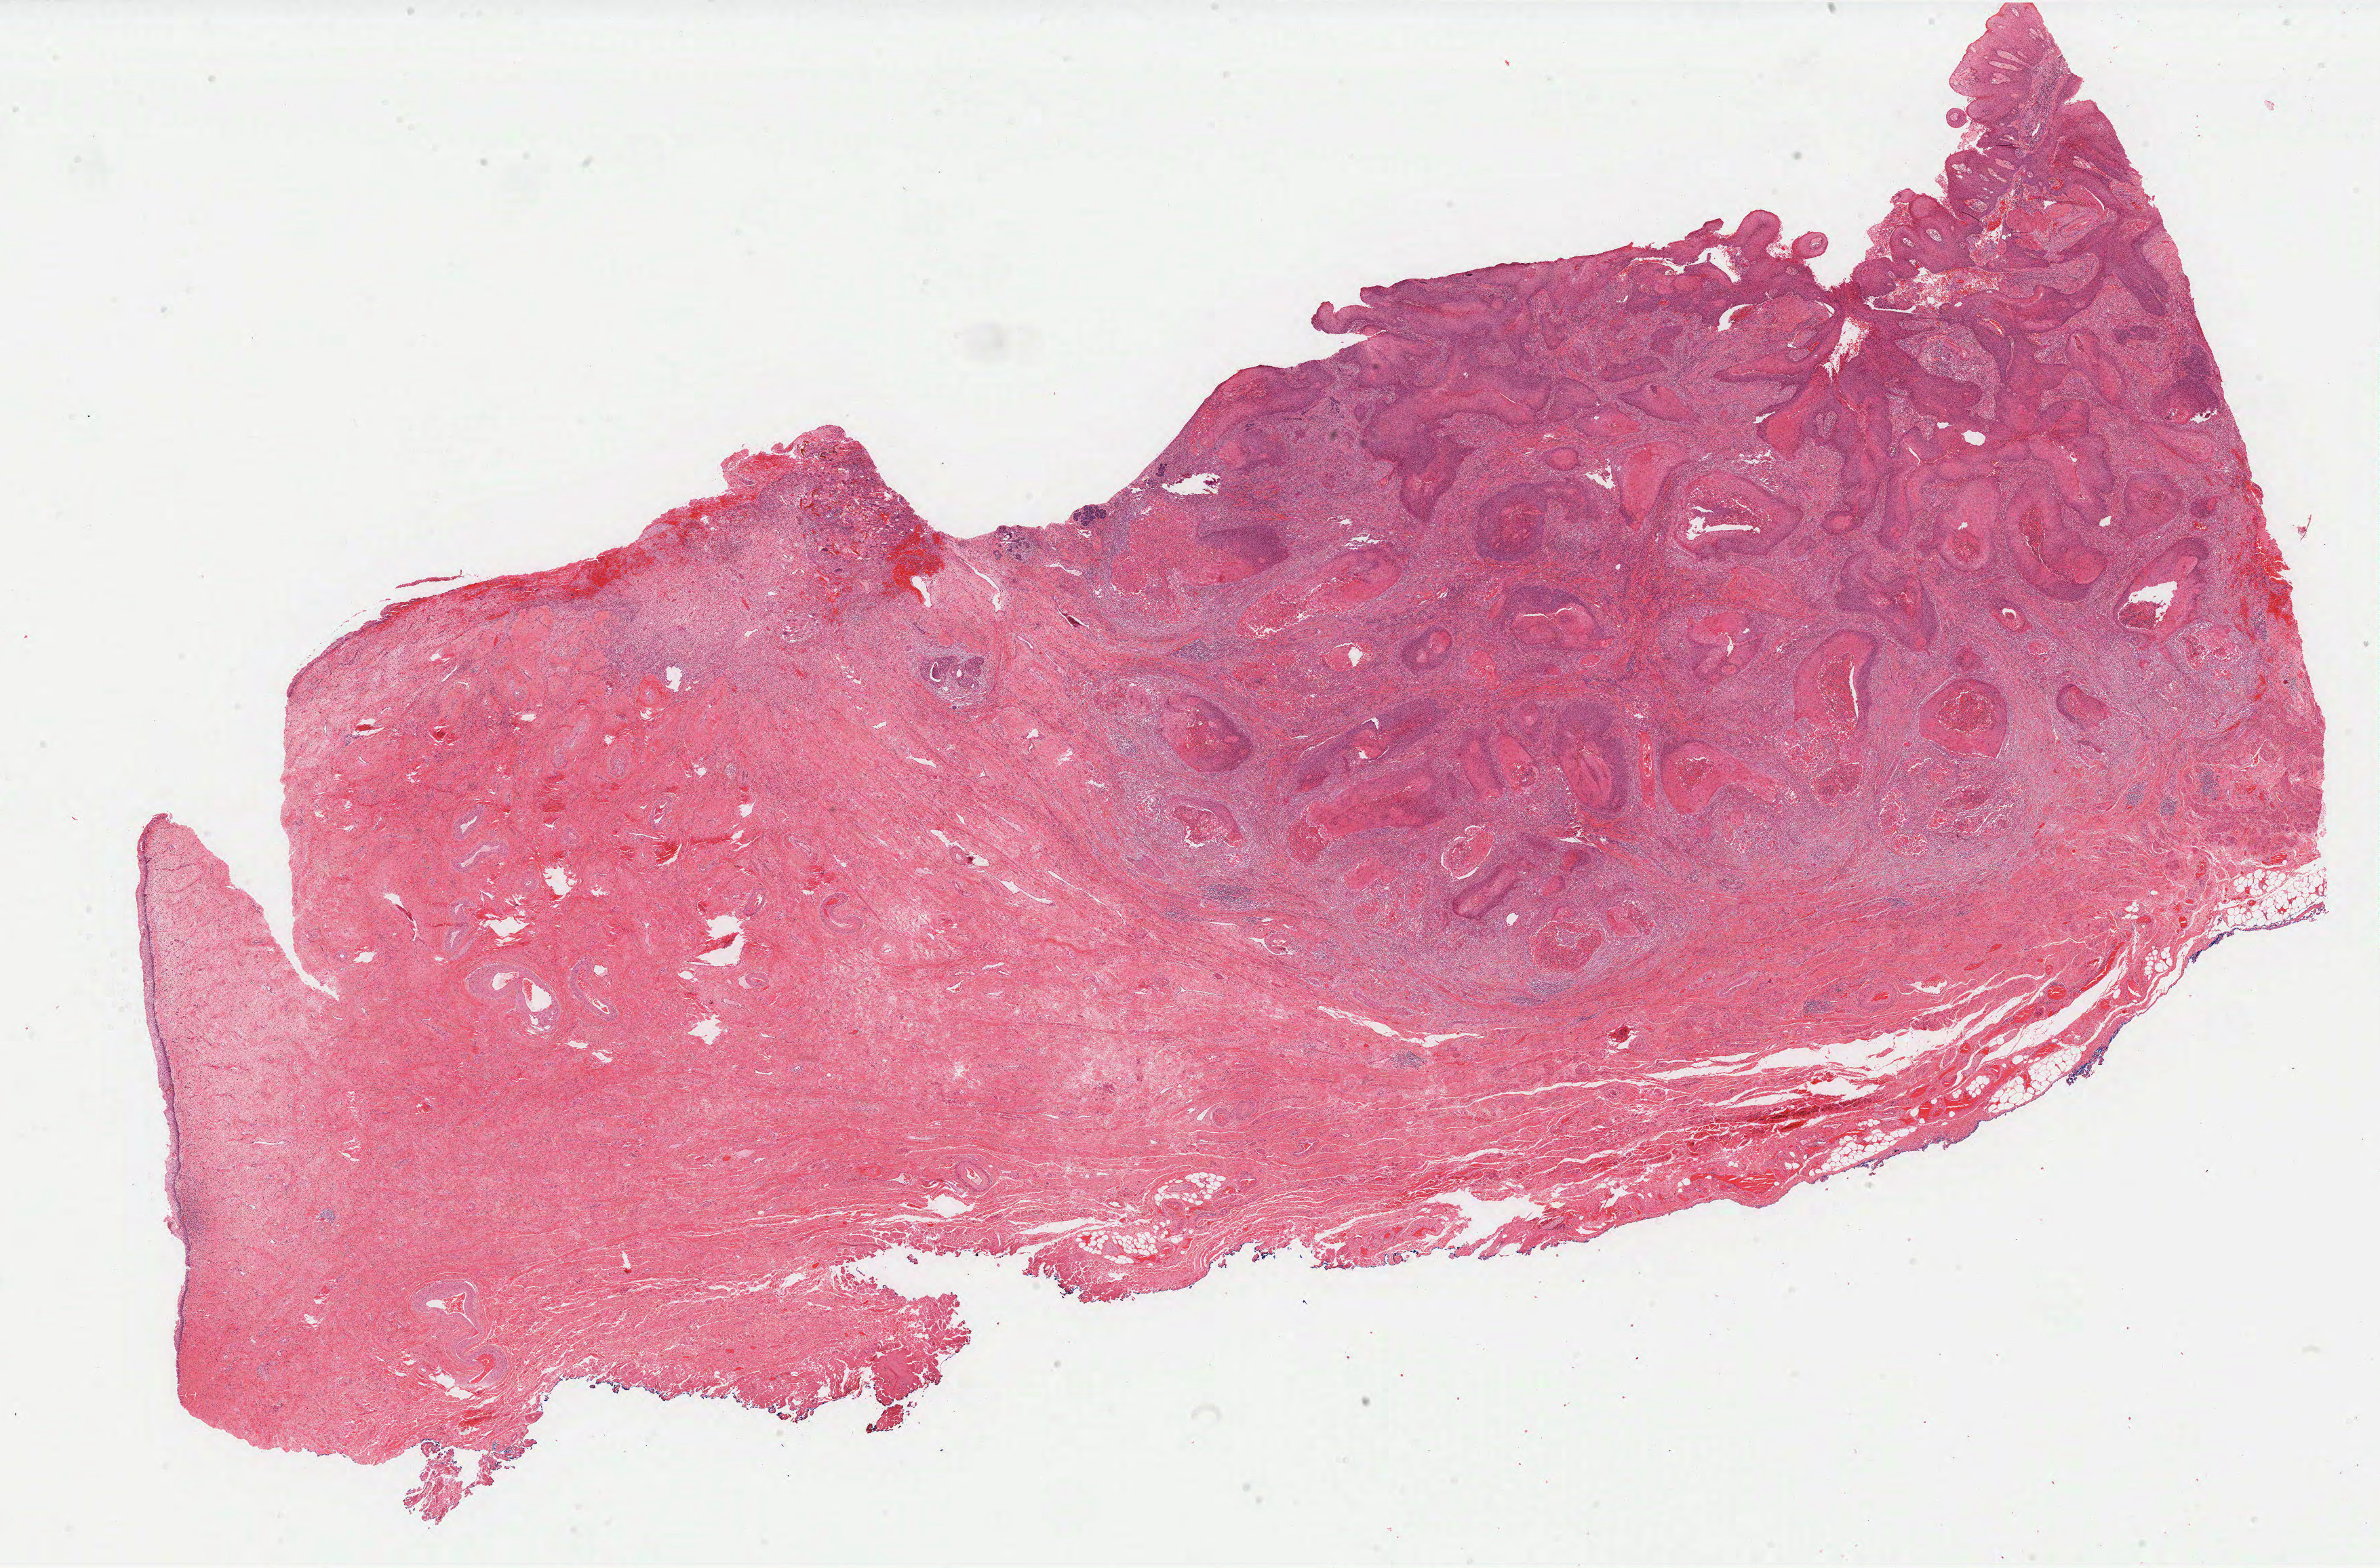
H&E whole-slide image, whole scanned area (about 28.1 x 18.5 mm, acquisition: 40x scan) shown as a low-resolution overview, formalin-fixed paraffin-embedded (FFPE) diagnostic section, primary tumour sample from the cervix. Patient: female, age at initial diagnosis 76 years. Histologic grade: G2 (moderately differentiated).
Lymph nodes positive (case pathology): 0 of 21 examined. FIGO stage: IB2. Pathologic diagnosis: Squamous cell carcinoma, keratinizing, NOS (cervix uteri).